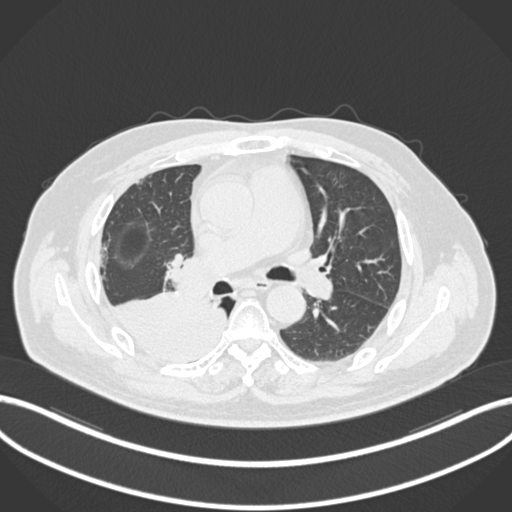
Chest CT, one axial slice. Slice 111 of 218 in the series (ordered by position). 120 kVp. Lung window (W 1500 / L -600 HU). 1 mm slice thickness. 512 × 512 image matrix, field of view 400 × 400 mm. Patient: male, 68 years. From the clinical record (not read from this slice): clinical TNM (as recorded): T2a N0 M0.
Structures marked on this image (bounding box drawn by a radiologist):
- lung tumour (recorded histology: adenocarcinoma): bounding box [x1, y1, x2, y2] px = [109, 285, 232, 371]